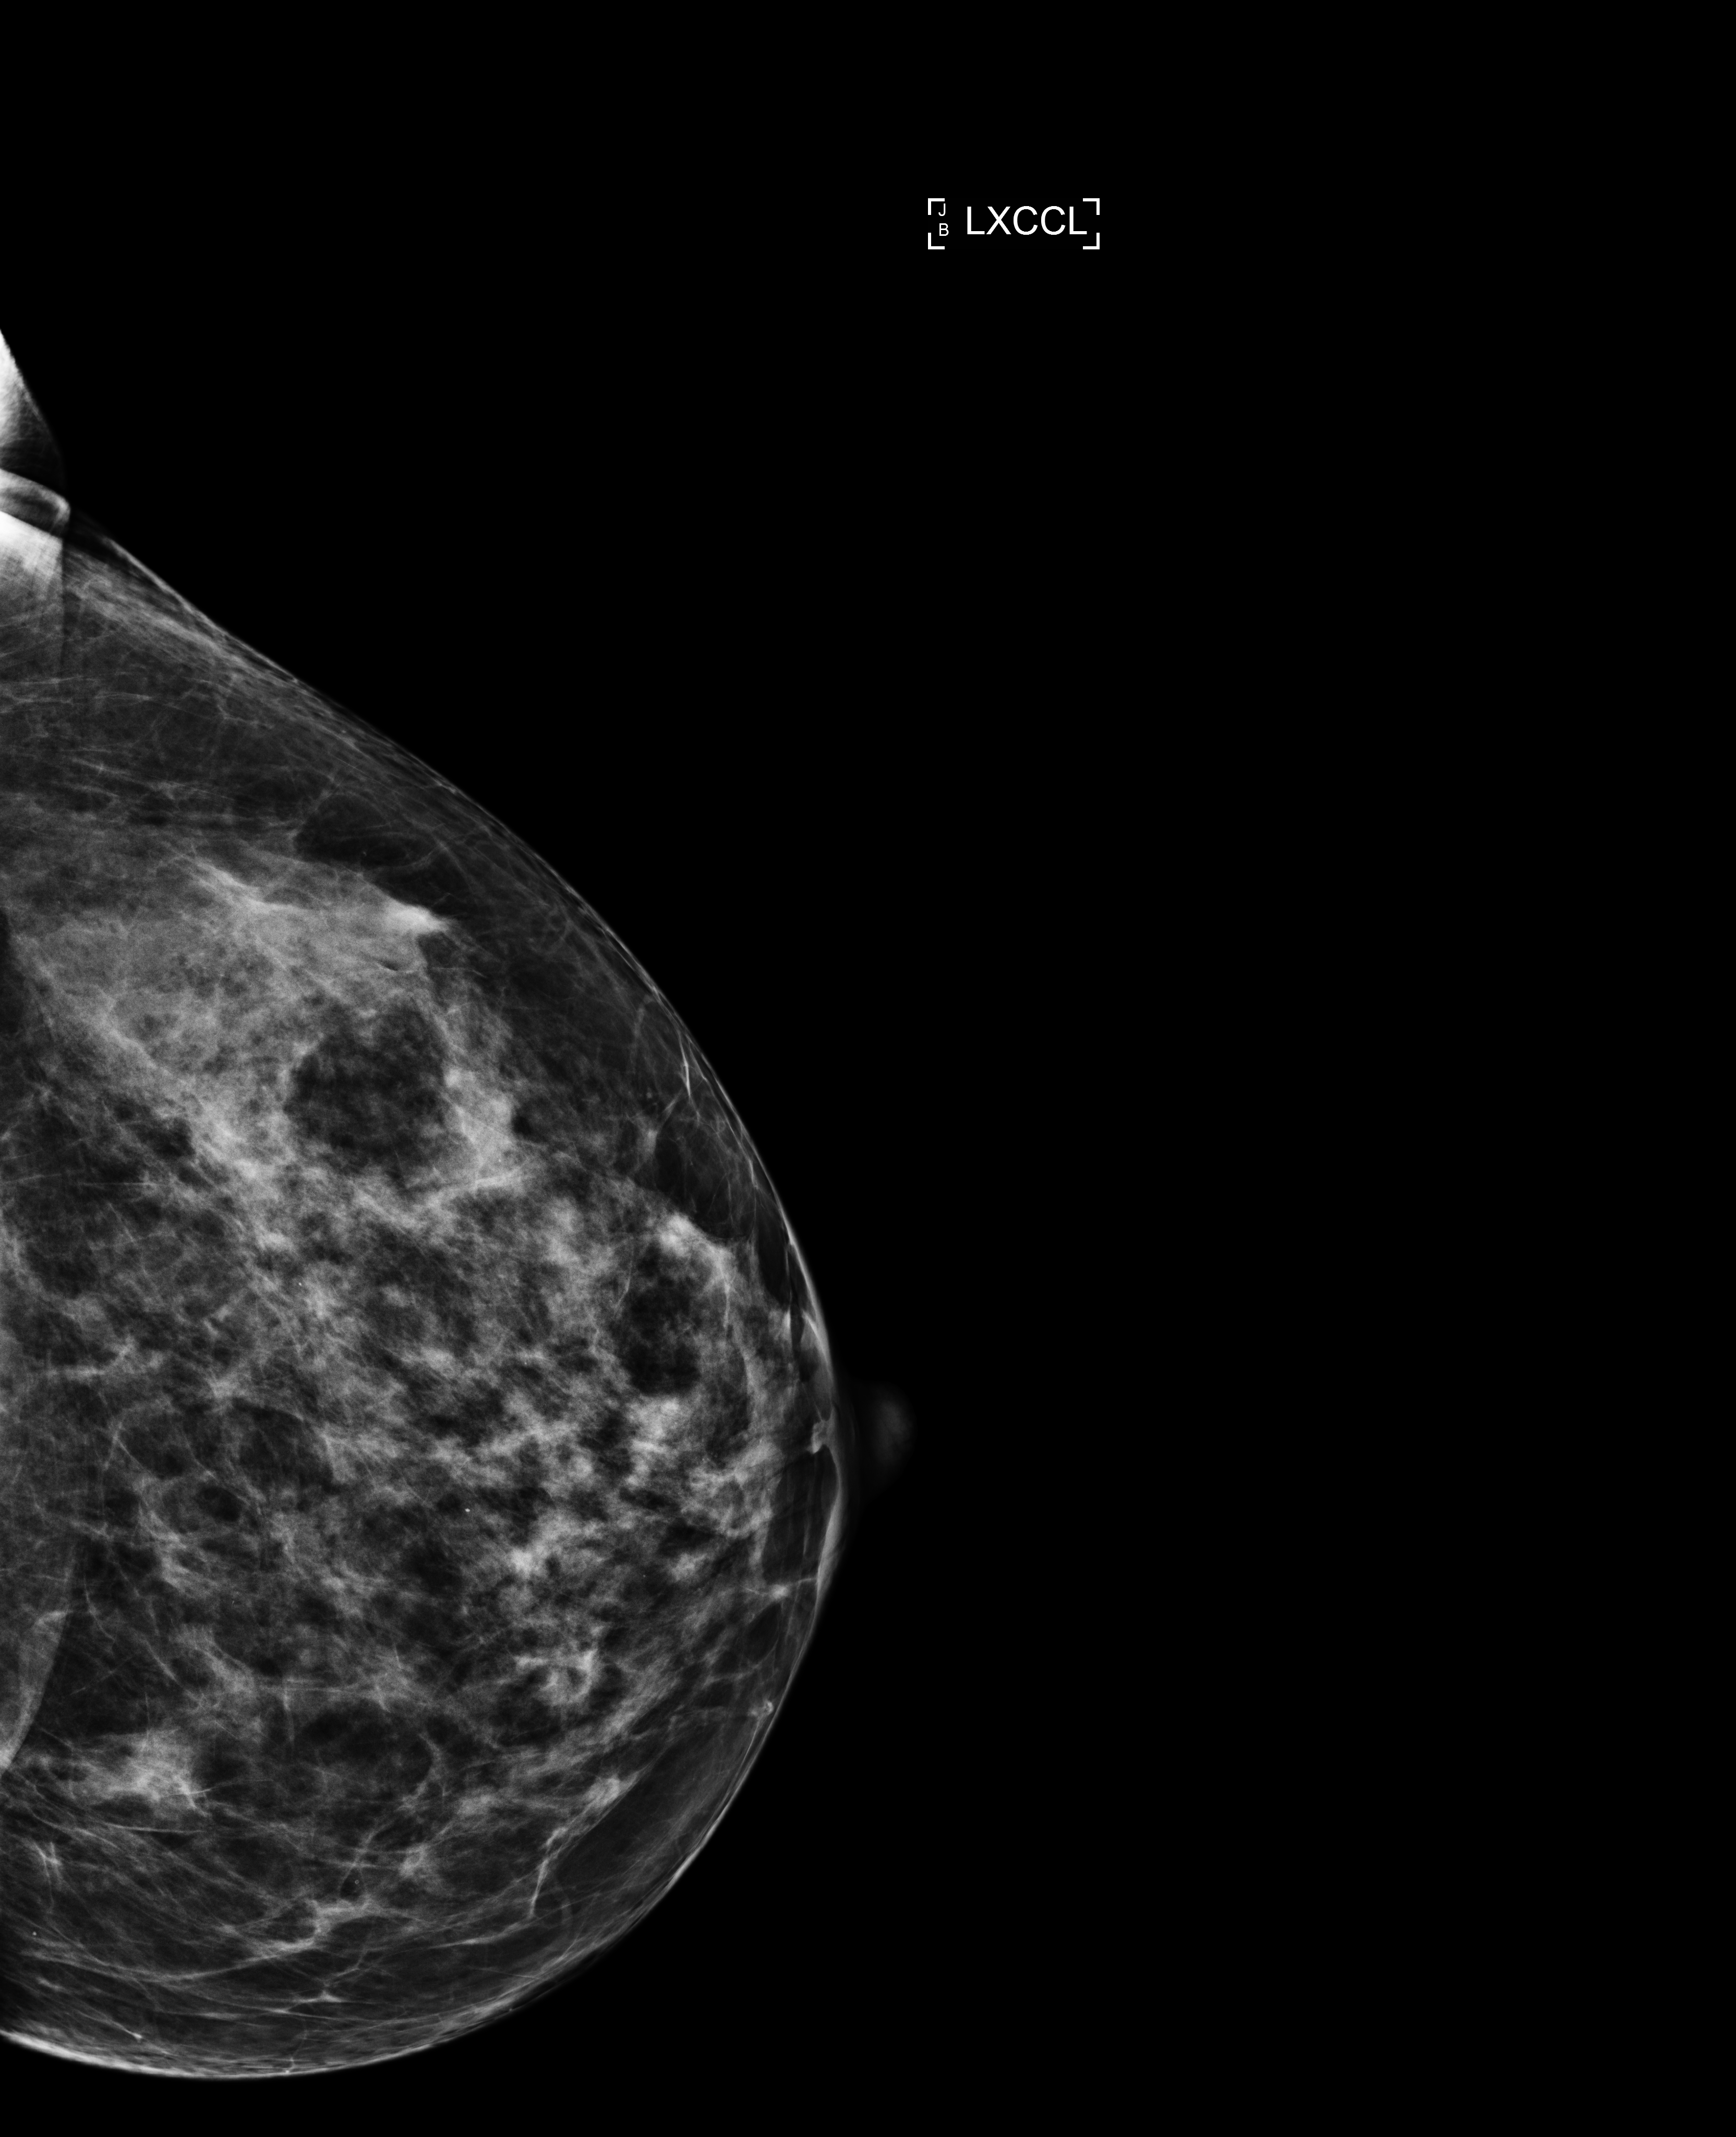
Screening examination; system: Selenia Dimensions. Female patient, age 47 years.
Image type: full-field digital mammogram. Breast: left. Projection: laterally exaggerated craniocaudal (XCCL) view. BI-RADS breast density category at the screening exam (both breasts, scale 1–4): 3. Final BI-RADS category for the screening round (tomosynthesis exam, both breasts): category 1. Recall: no recall after this screen.